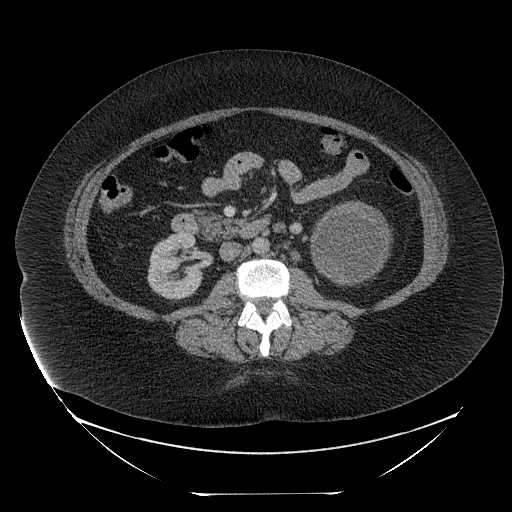
Contrast-enhanced abdominal CT, one axial slice; position 115 of 205 along the scan axis; intravenous contrast given; soft-tissue window (W 400 / L 40 HU); 512 × 512 image matrix. Female patient, age 53 years. Case-level facts recorded for this patient, not image findings: diagnosis: adrenocortical carcinoma; tumour side: left adrenal; tumour size at pathology: 17 cm; Ki-67 index: 20 %; stage (as recorded): 3.
Structures marked on this image (semi-automatic segmentation, software-assisted and operator-edited):
- mass: bounding box [x1, y1, x2, y2] px = [314, 204, 387, 282]